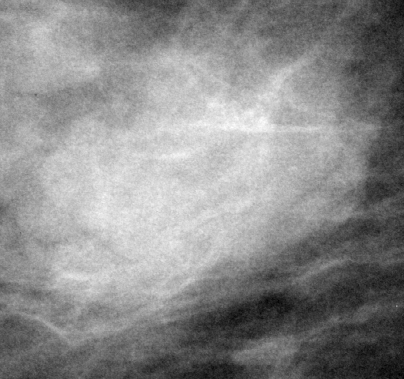
Cropped region of a digitized screen-film mammogram centred on a radiologist-marked abnormality, right breast, MLO view.
- Mass, shape lobulated, margins circumscribed; BI-RADS assessment category 4; subtlety rating 5 on a 1 (subtle) to 5 (obvious) scale; pathology (as recorded): benign.